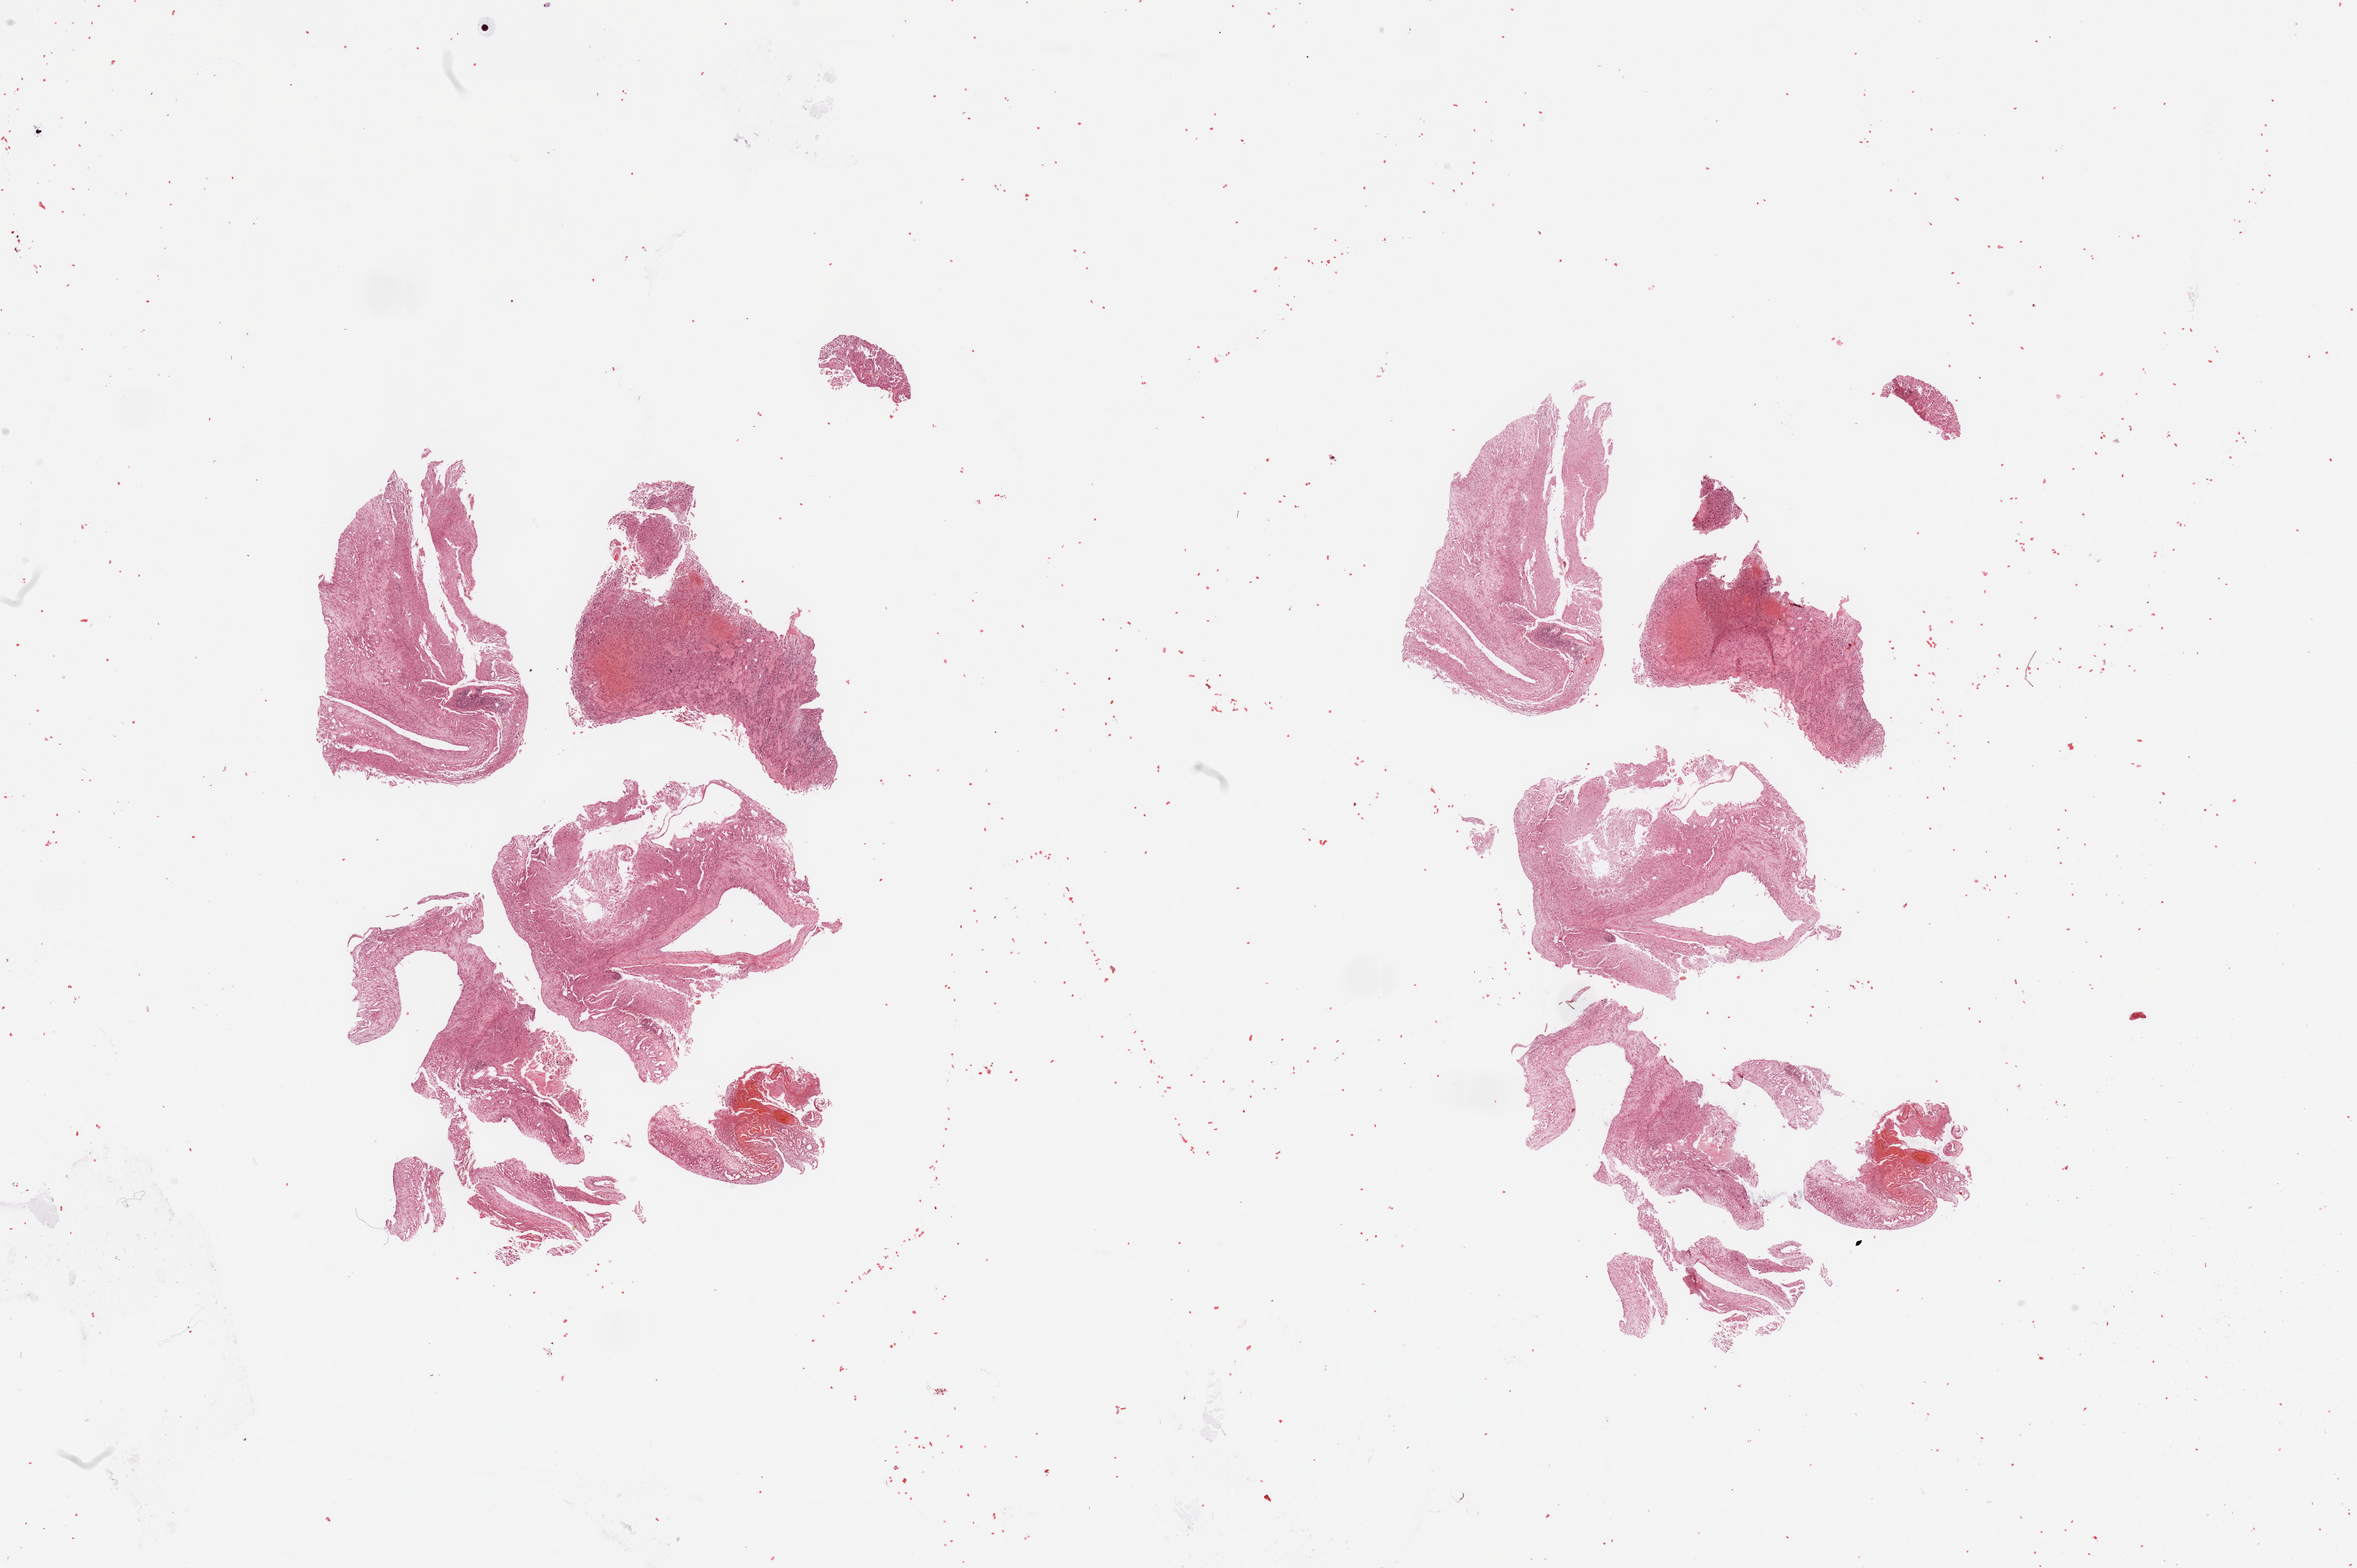
H&E whole-slide image — whole scanned area (about 28.5 x 19.0 mm) shown as a low-resolution overview; tumour tissue sample, brain. Patient: male, age 49 years.
Primary tumour site (as recorded): temporal lobe. Diagnosis: Glioblastoma.